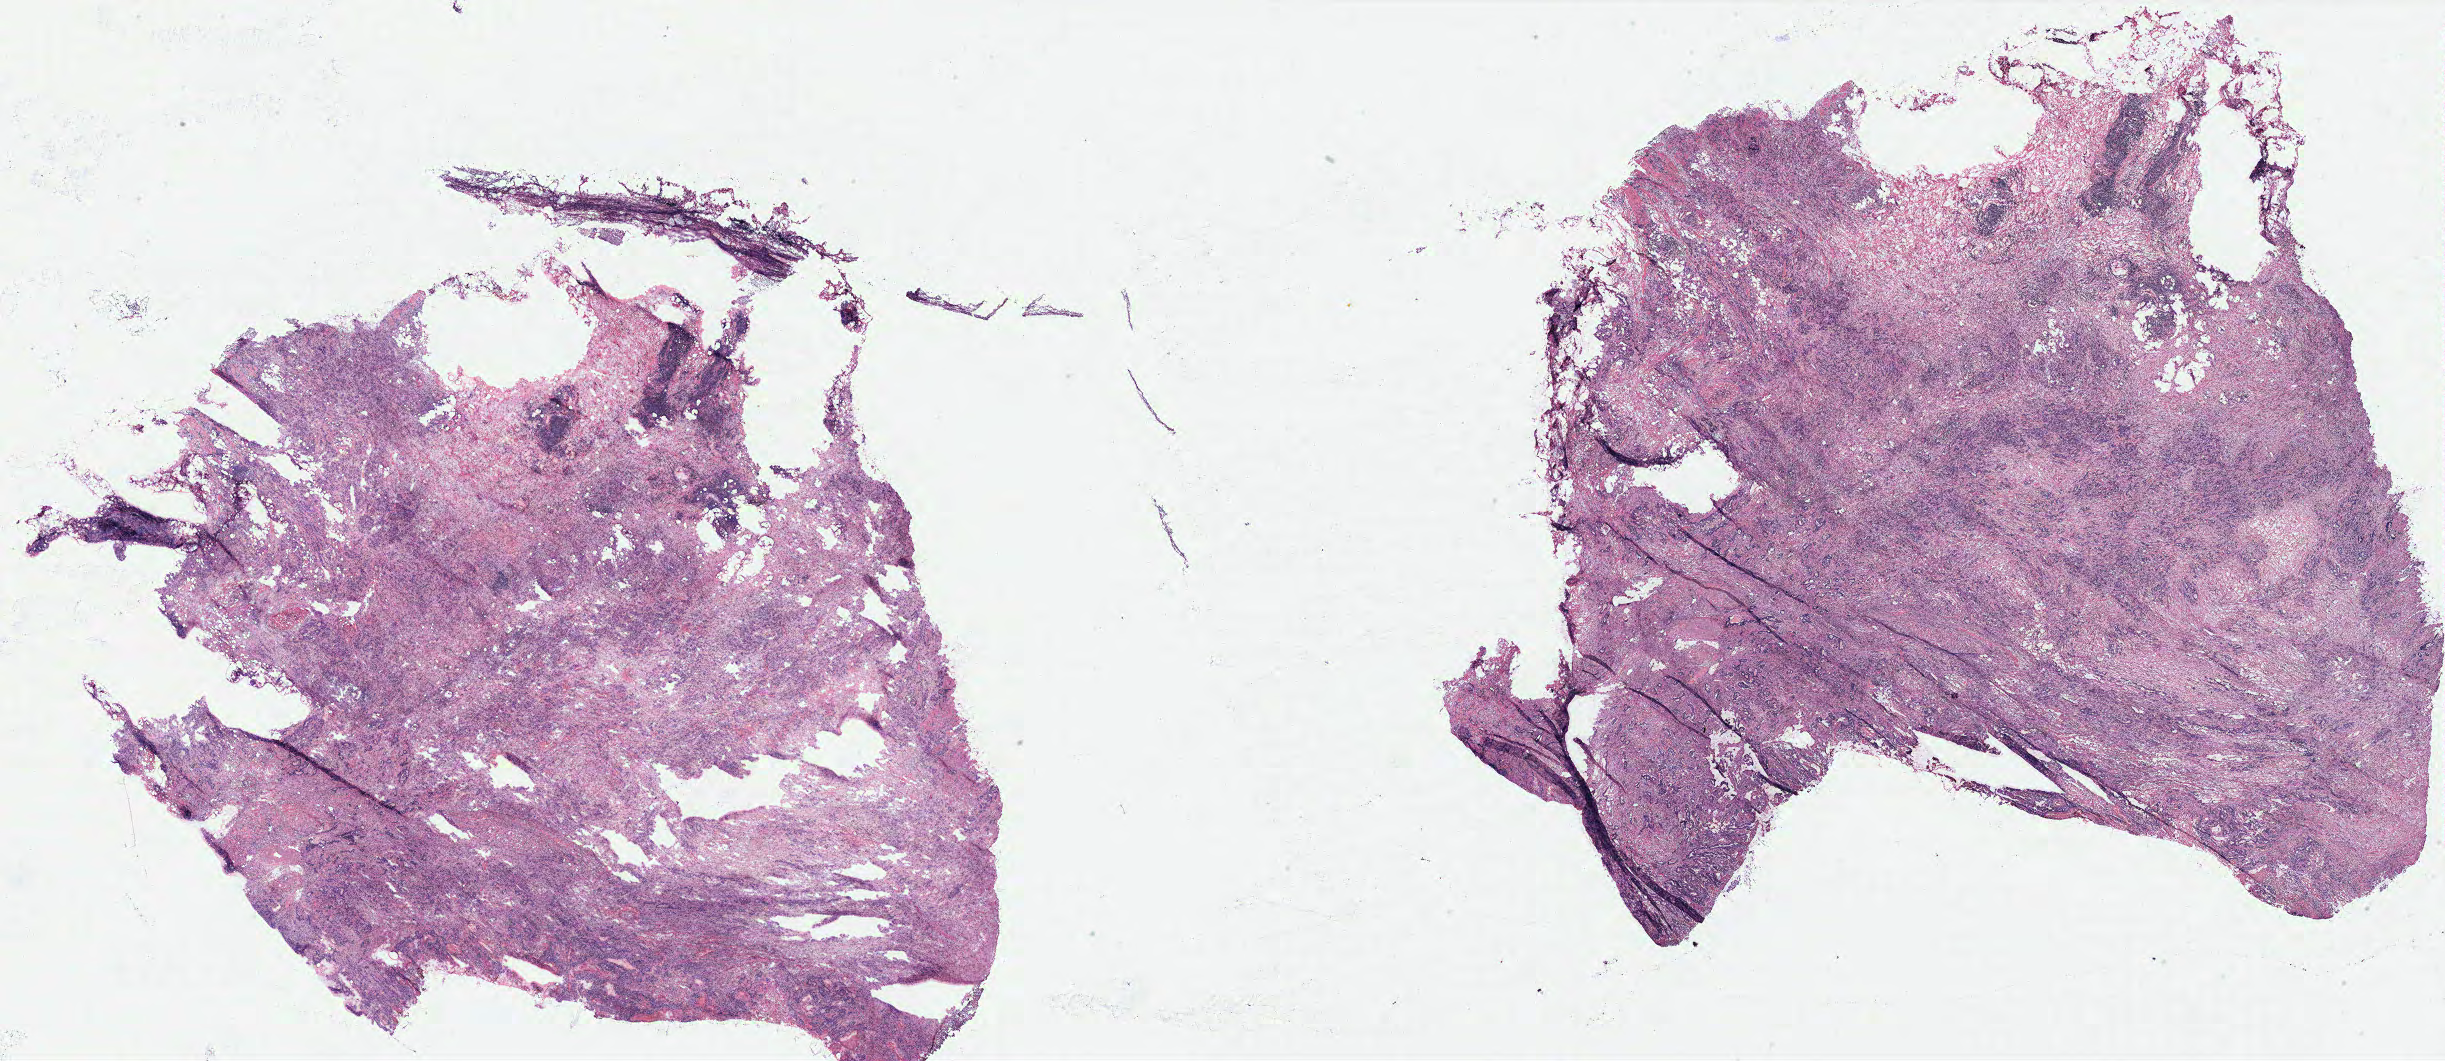
Whole-slide histology image, H&E-stained — shown as a low-resolution overview of the whole scanned area (about 39.1 x 17.0 mm); colon, tissue type not recorded.
Patient diagnosis (cohort enrolment): colon cancer (colon).